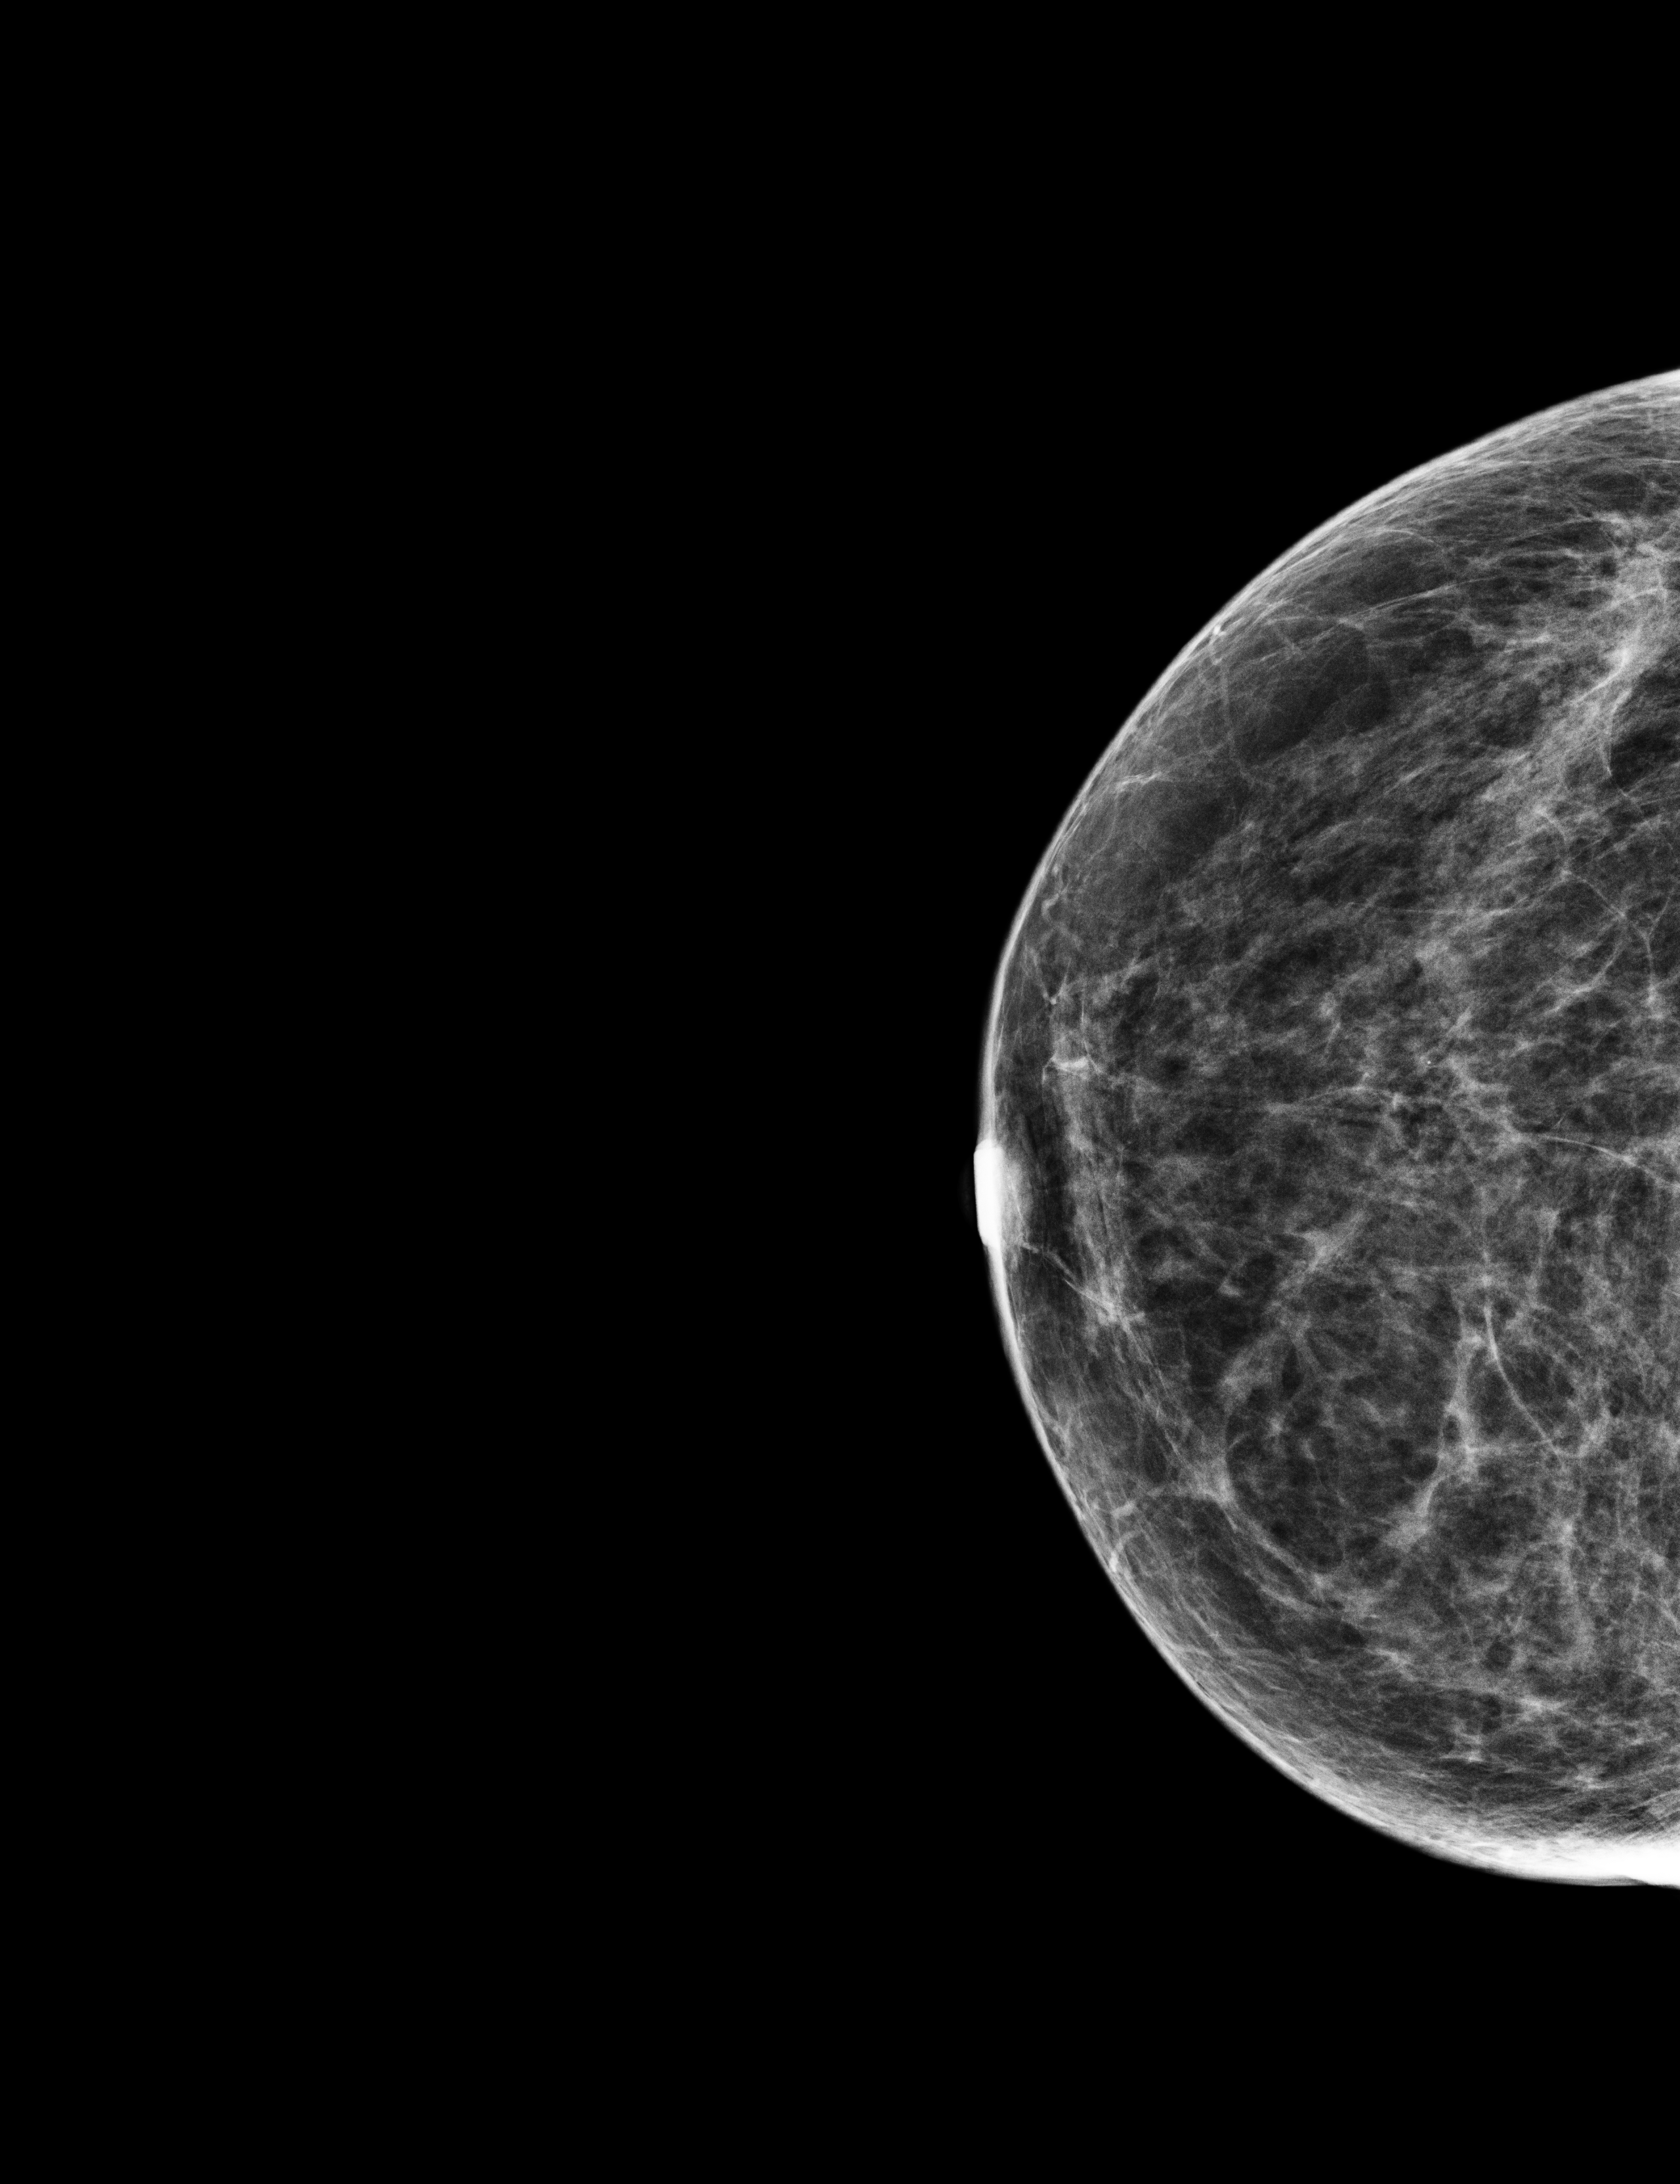
Digital mammogram (FFDM); right breast; craniocaudal (CC) view; screening examination. Female patient, age 64 years.
Breast density at the screening exam (both breasts): heterogeneously dense (BI-RADS density category c). Final BI-RADS assessment for this screening round (tomosynthesis exam, both breasts): category 1. Recall: no recall after this screen.